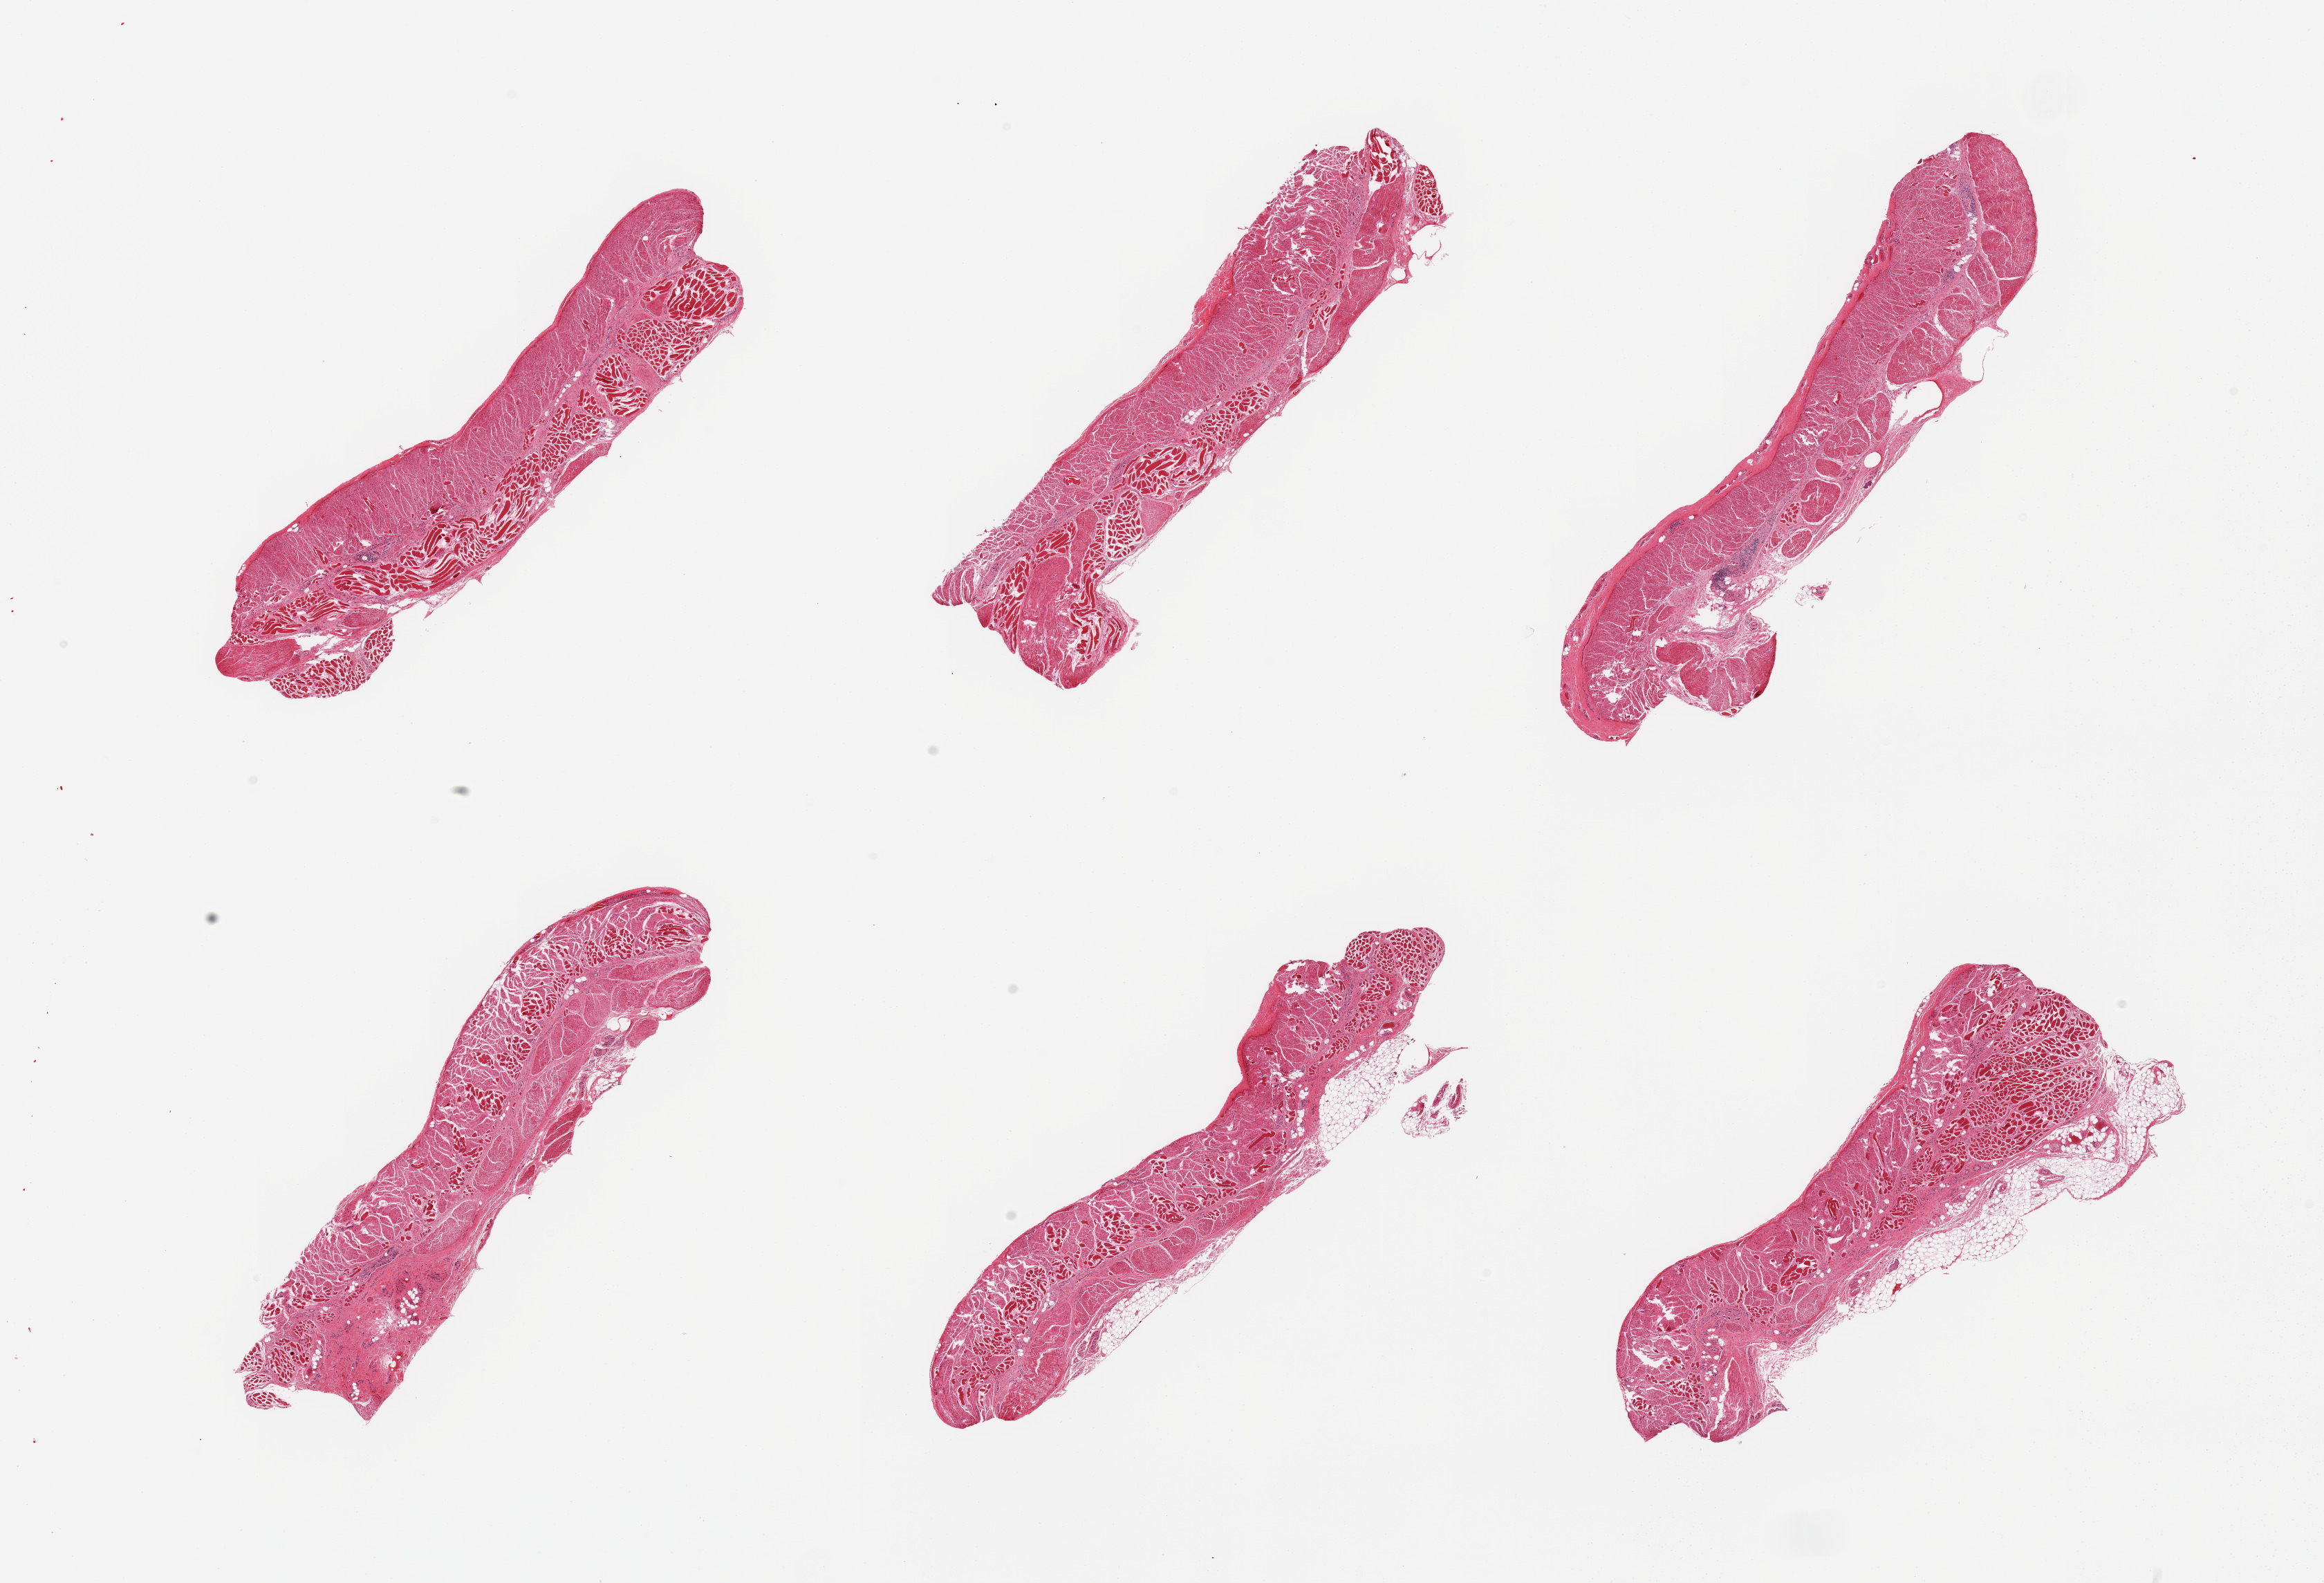
Whole-slide image, H&E stain, a low-resolution overview of the entire scanned area, about 26.6 x 18.1 mm (acquisition: 20x scan); PAXgene-fixed paraffin-embedded (PFPE) section; target tissue: esophageal muscle; donor tissue sample.
Review note (as recorded): 6 pieces; admixture of smooth muscle and skeletal muscle, two pieces with 10-20% attached fat.